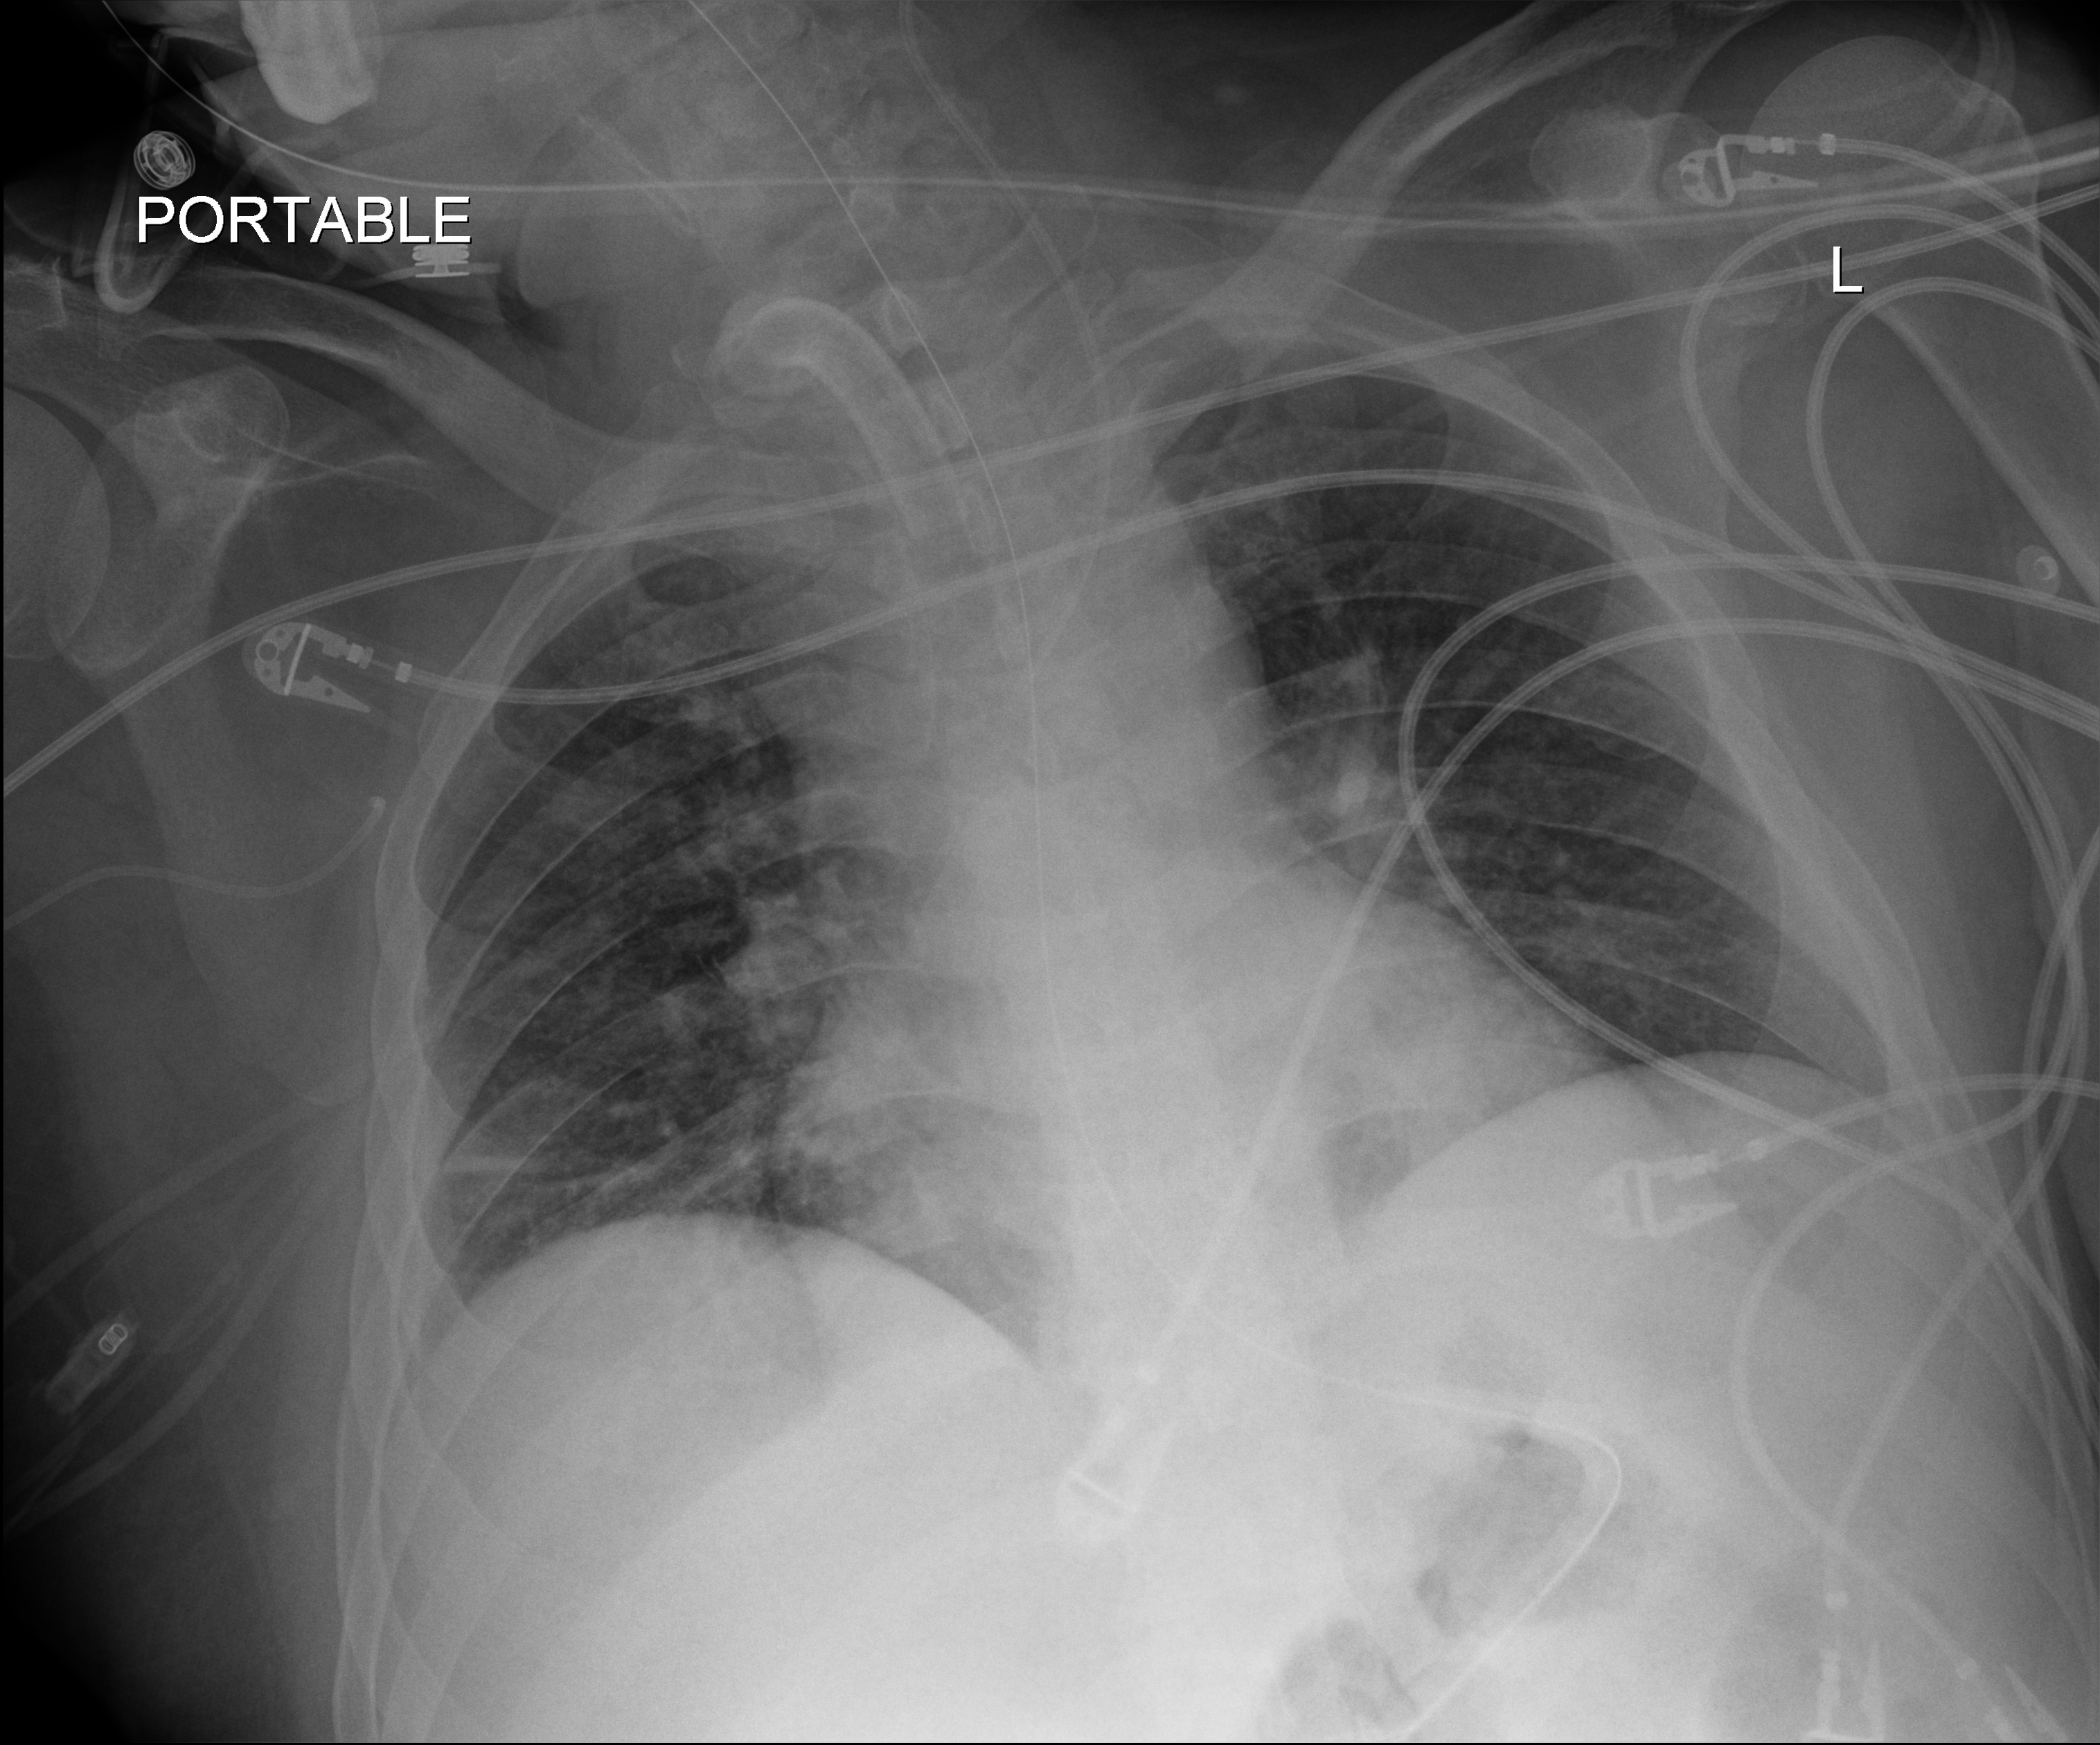
Bedside chest radiograph (digital radiography), anteroposterior (AP) projection. Patient hospitalised with COVID-19; male, aged 18–59 years.
From the hospital-stay record, not from the radiograph (when in the stay this image was taken is not recorded):
- admitted to intensive care during this hospital stay: yes
- mechanically ventilated during this hospital stay: yes
- length of hospital stay: 65 days